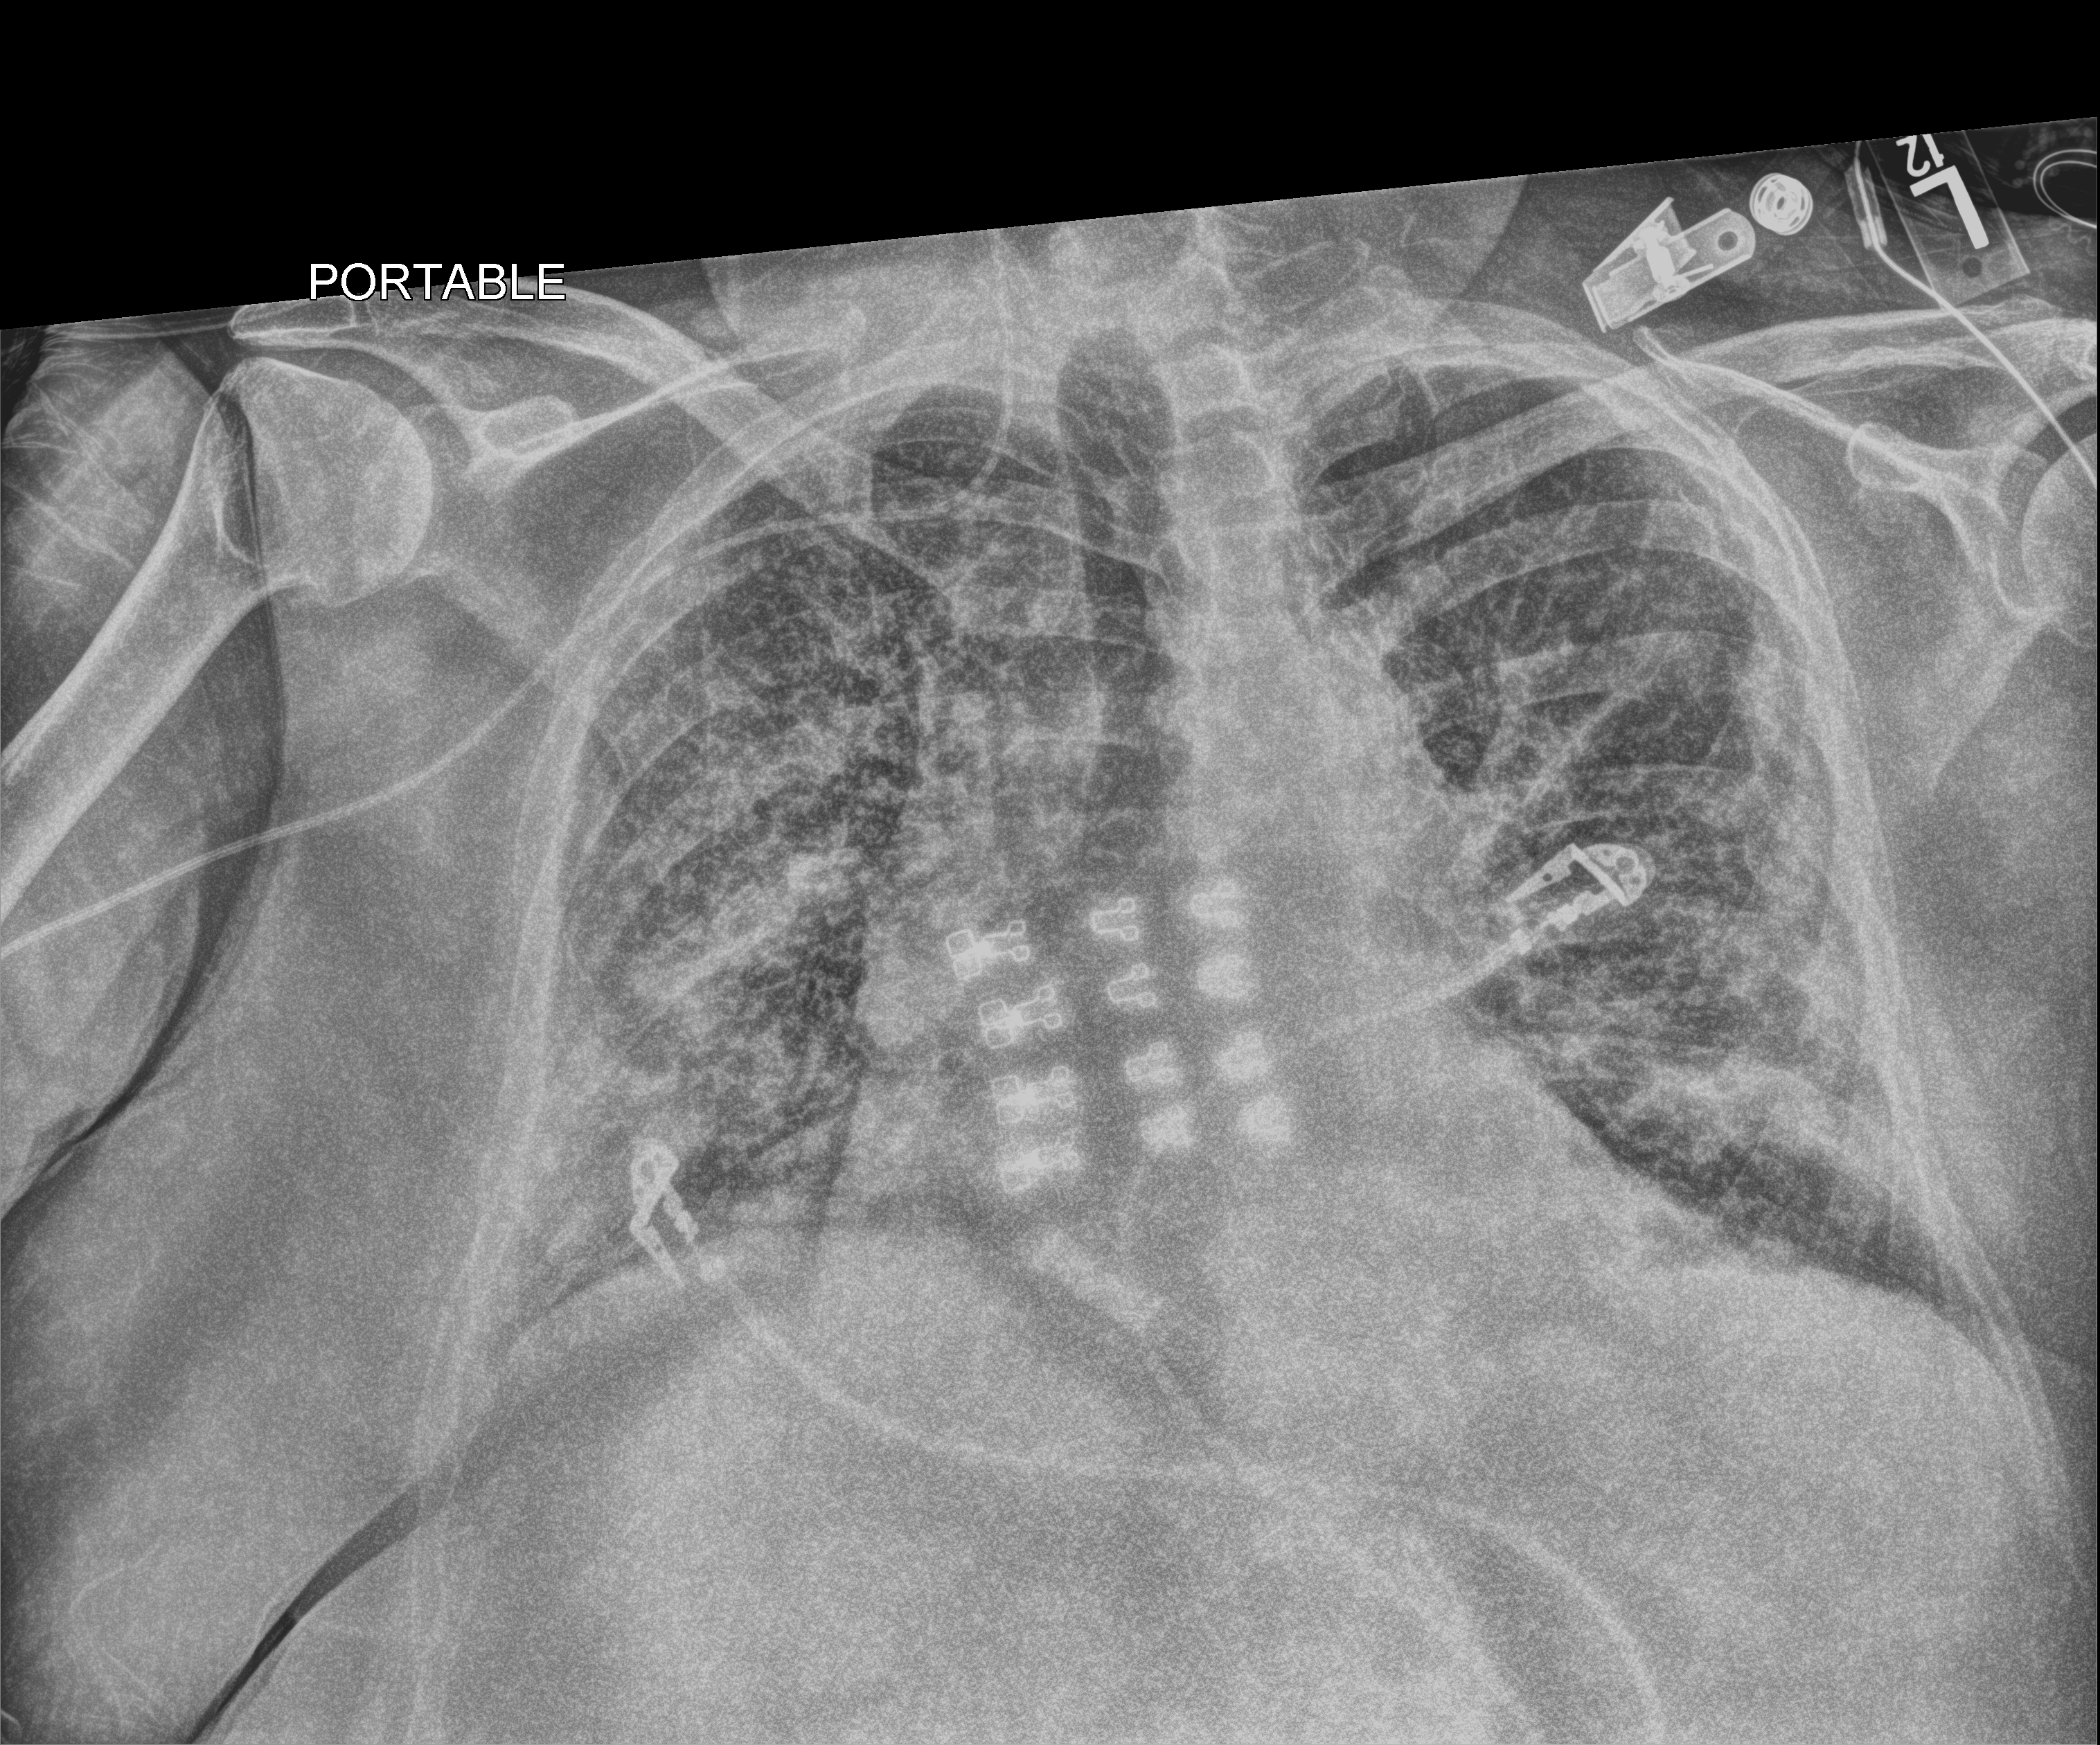
Bedside chest radiograph (computed radiography), anteroposterior (AP) projection. Female patient hospitalised with COVID-19, age 60–74 years.
From the hospital-stay record, not from the radiograph (when in the stay this image was taken is not recorded):
- admitted to intensive care during this hospital stay: yes
- mechanically ventilated during this hospital stay: yes
- diabetes (admission record): yes